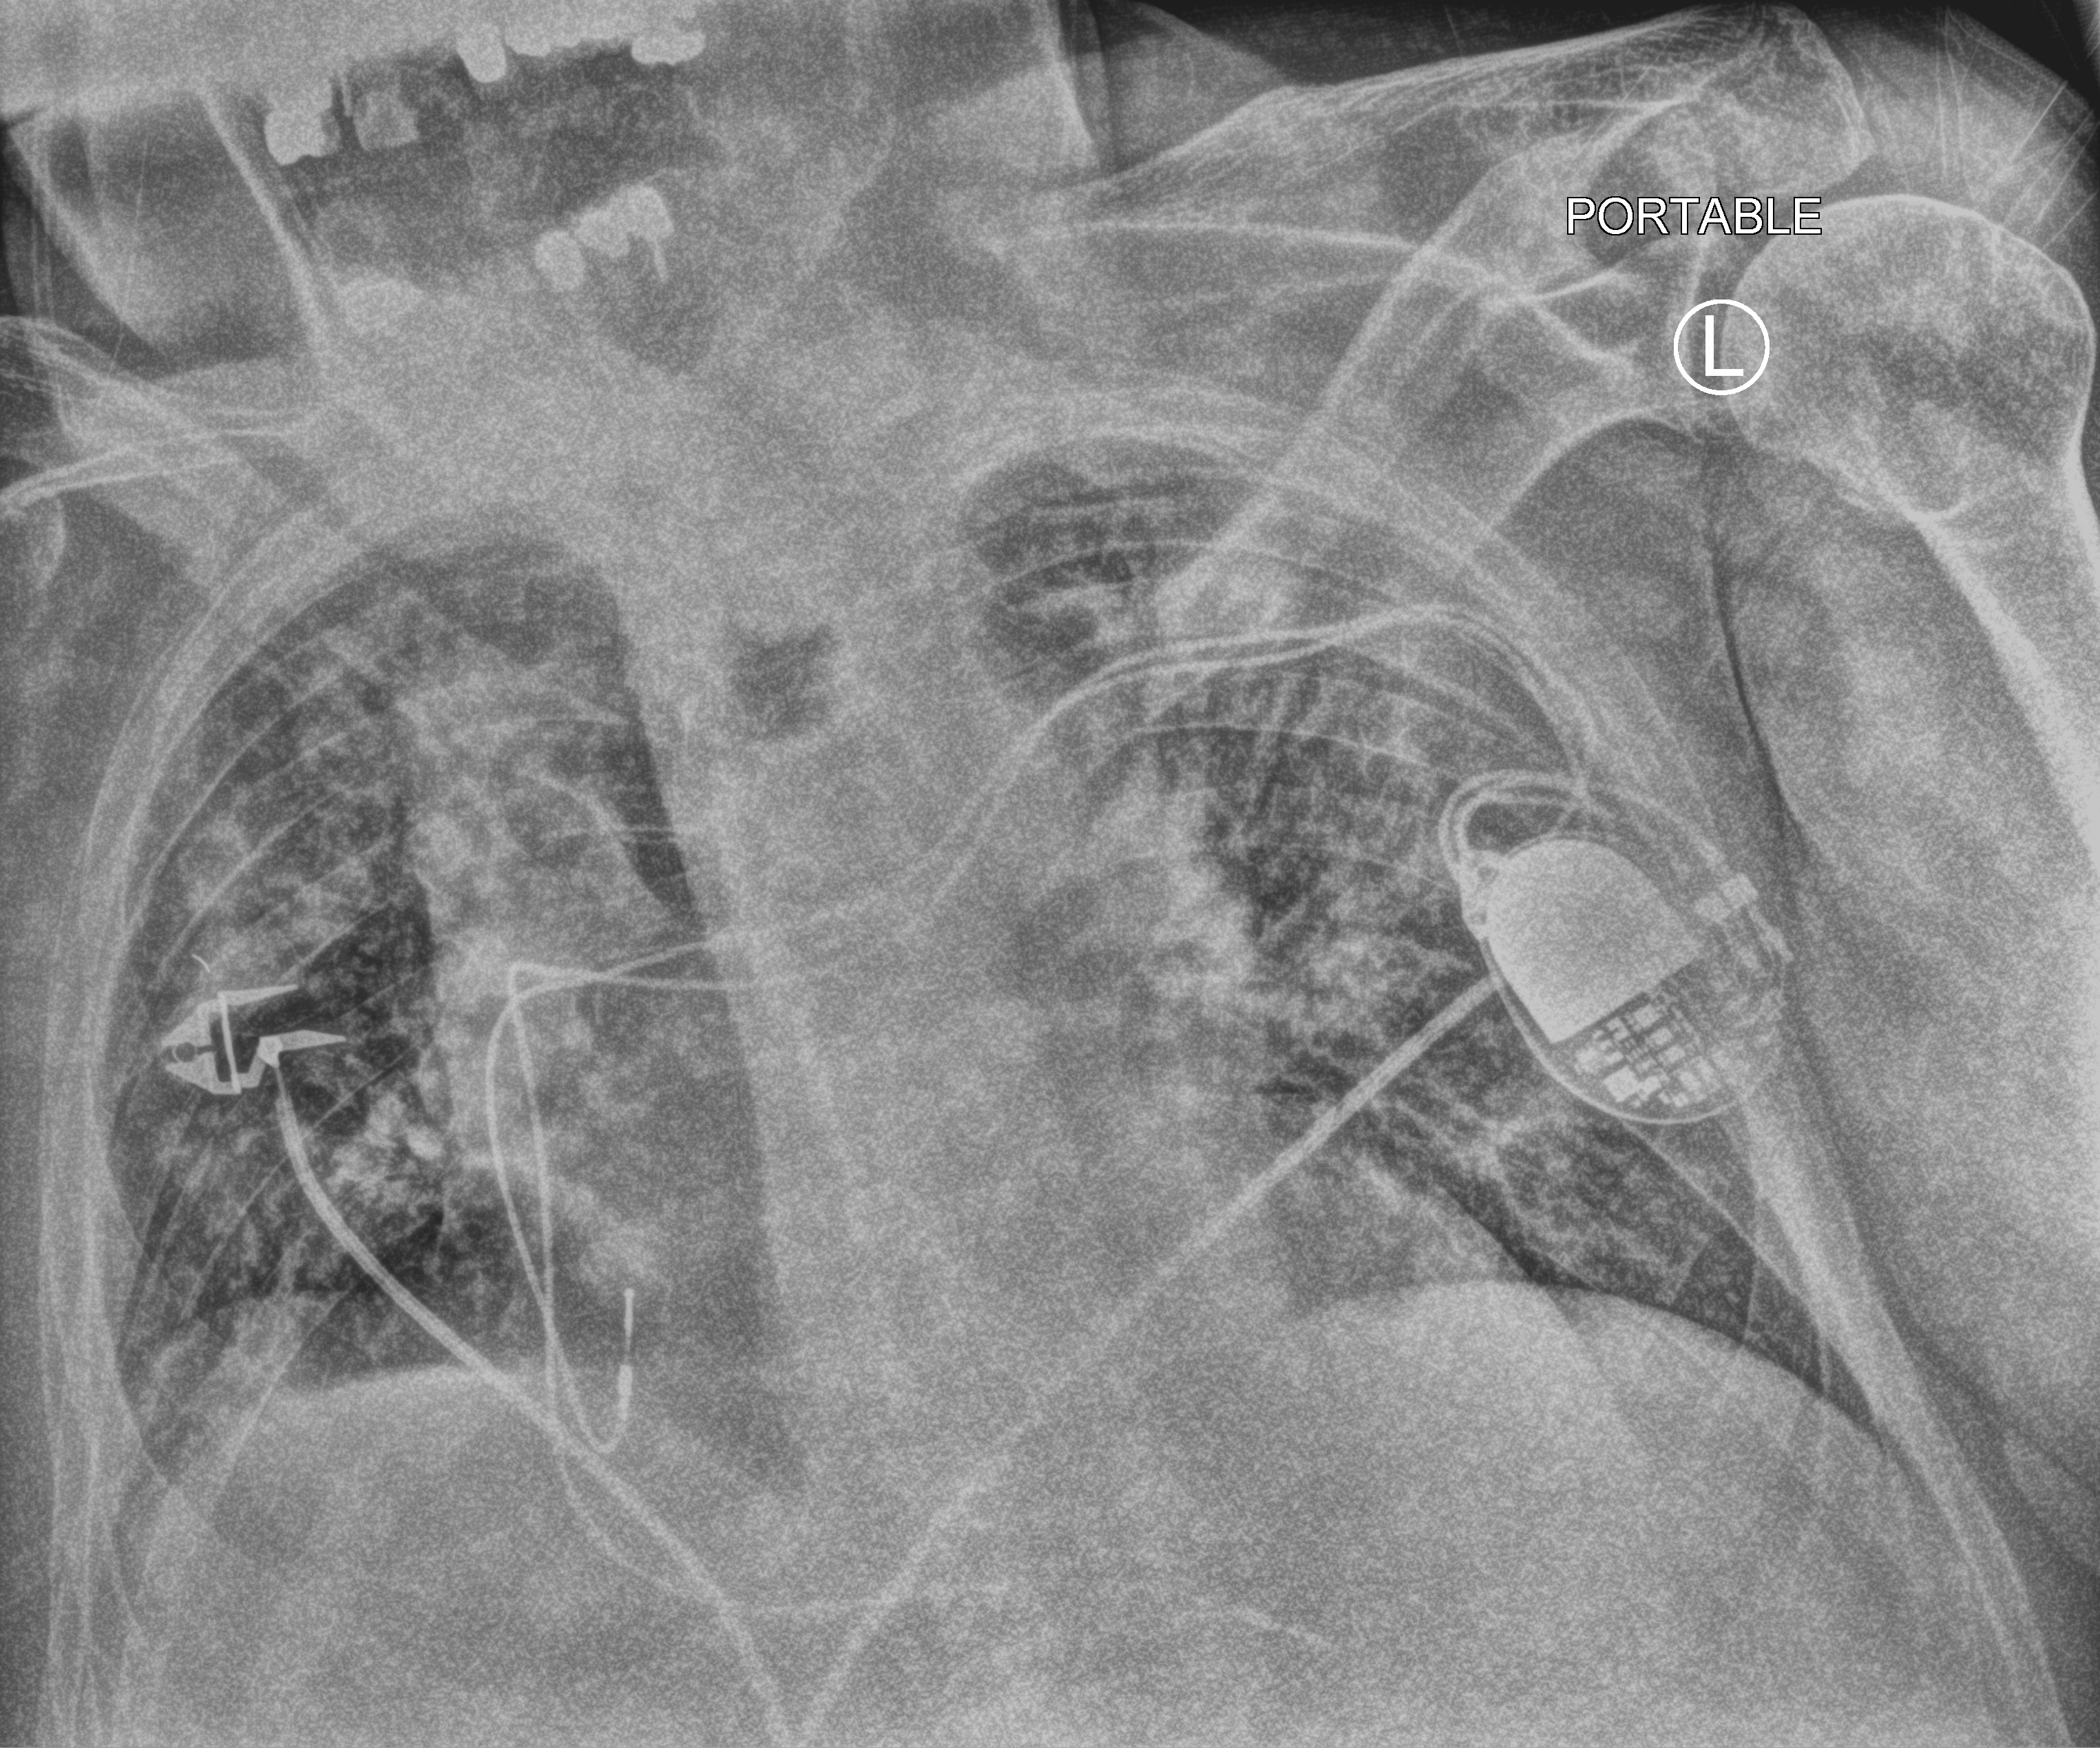
Bedside chest radiograph (computed radiography), anteroposterior (AP) projection. Male patient hospitalised with COVID-19, age 75–90 years.
Admission-level facts for this patient (not findings on this image; timing relative to this image not recorded):
- length of hospital stay: 15 days